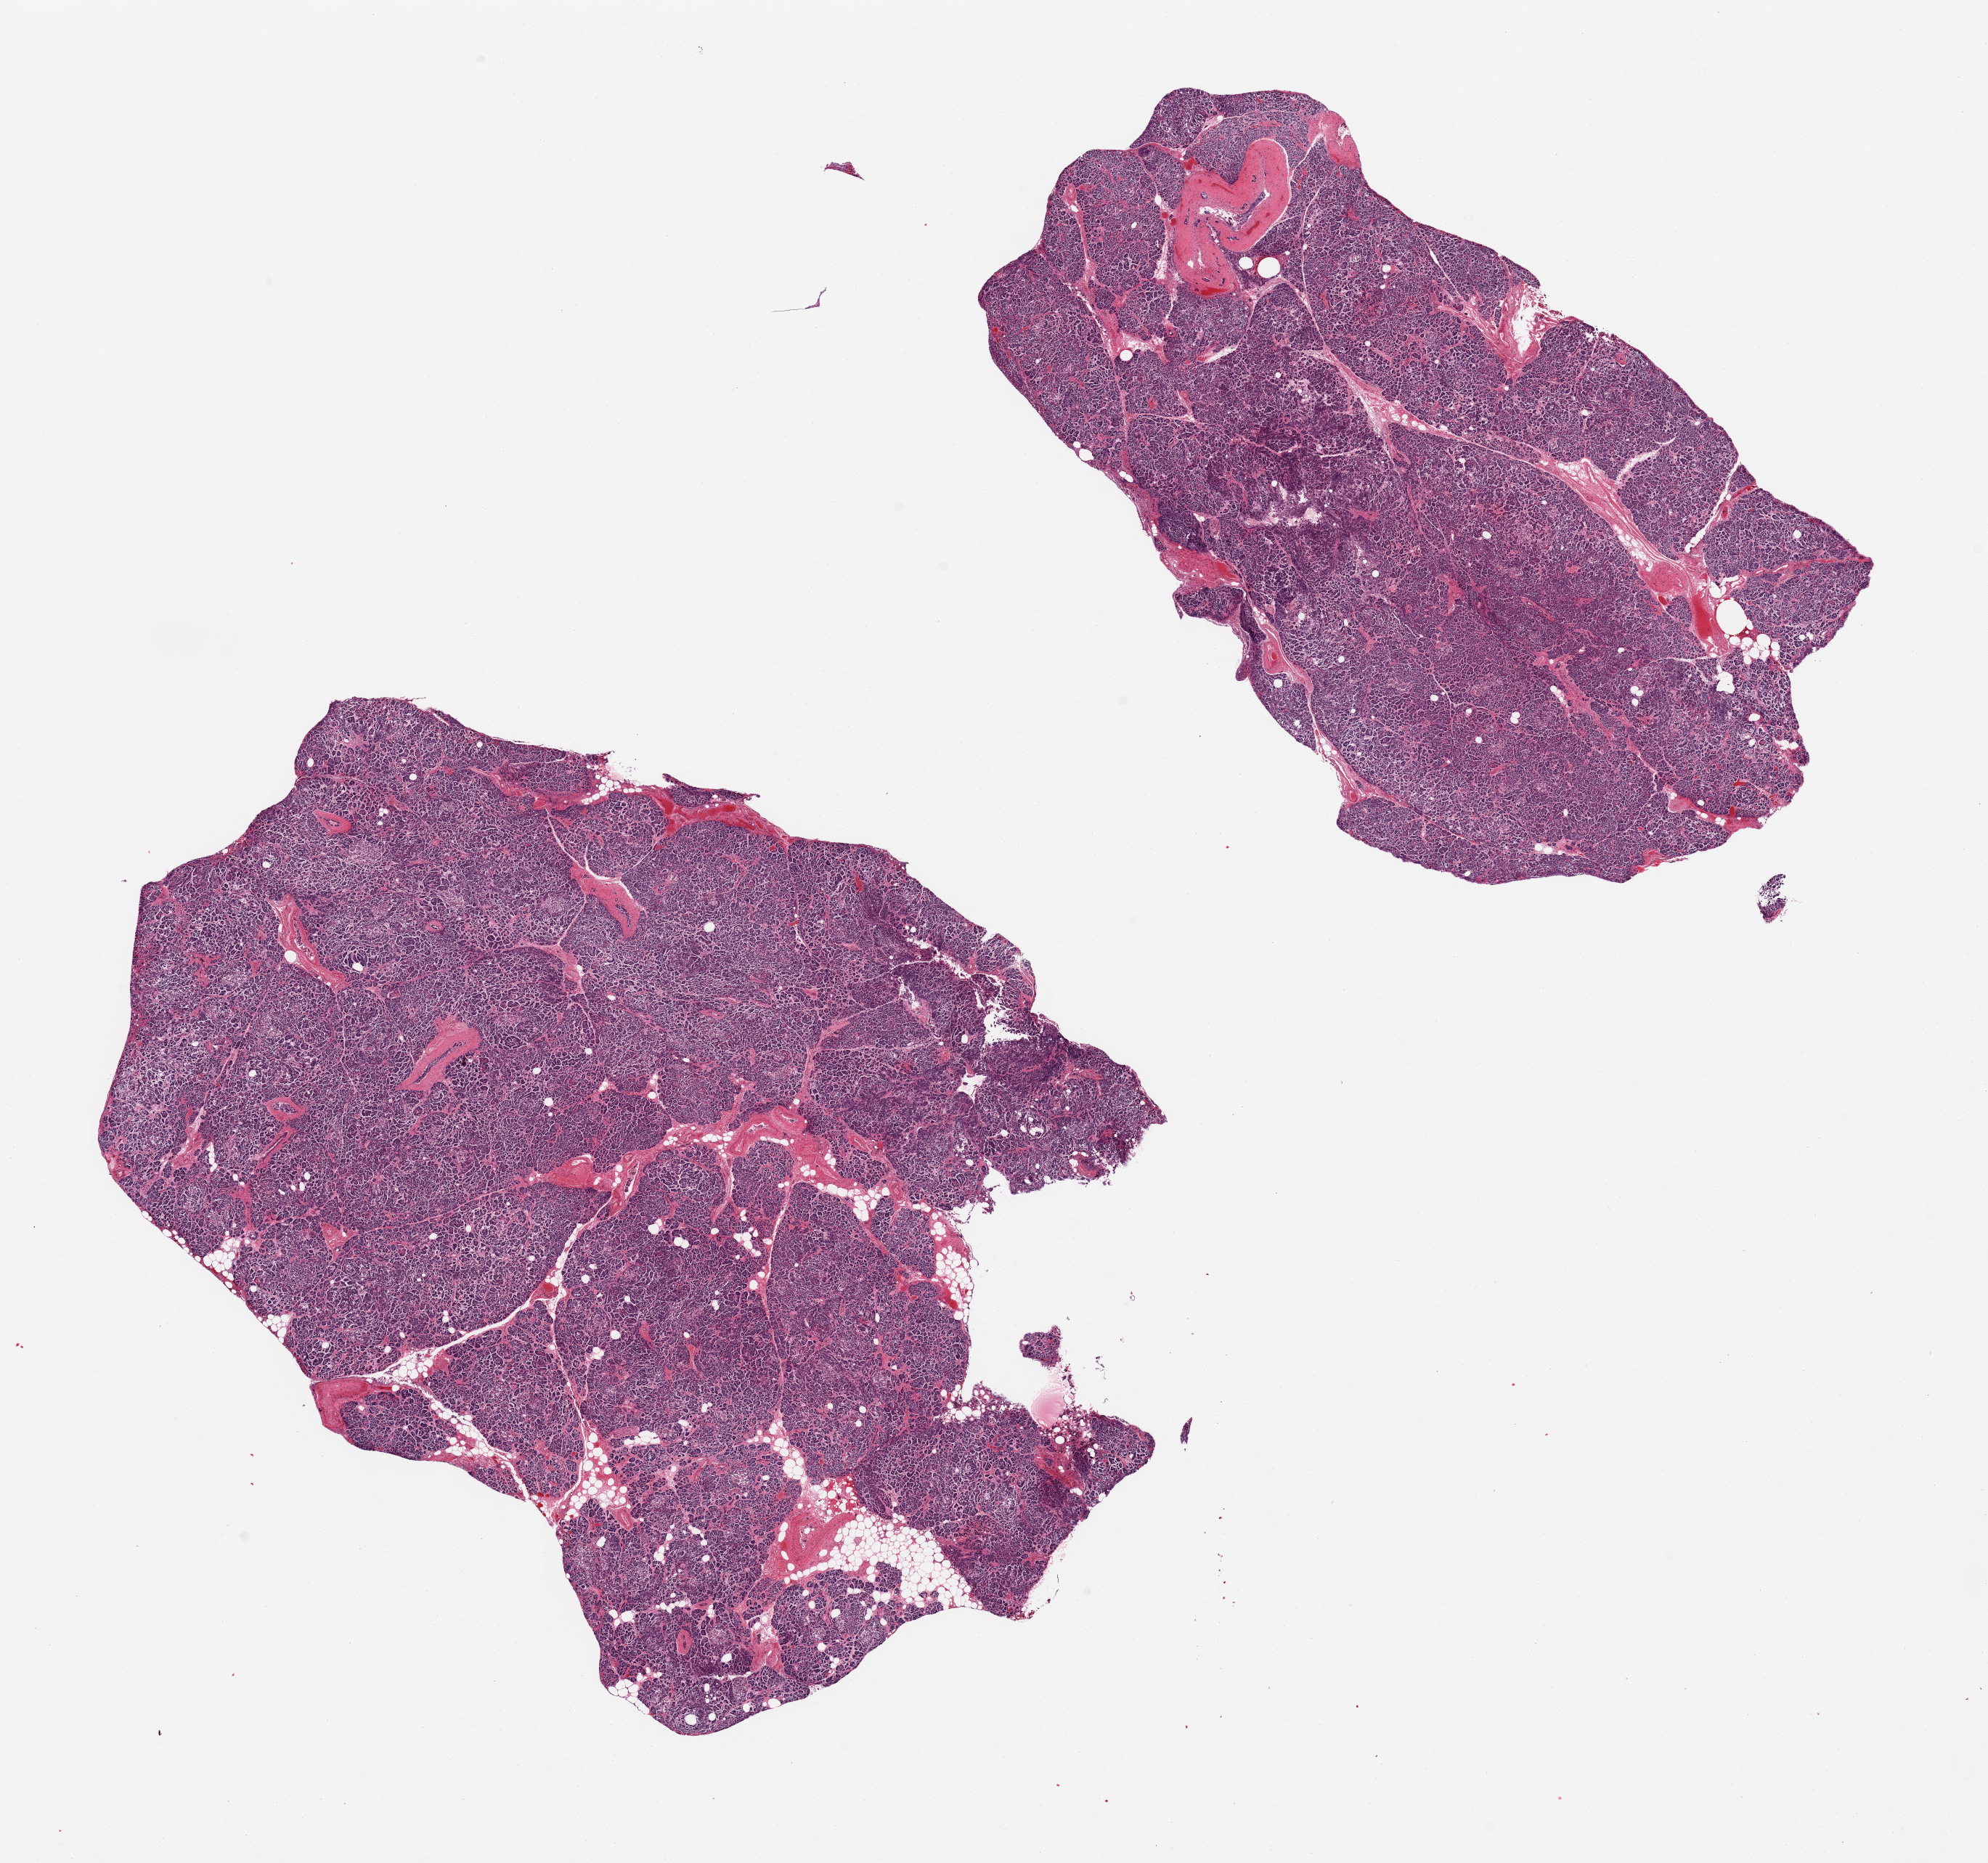
Digitized haematoxylin and eosin-stained section — shown as a low-resolution overview of the whole scanned area (about 21.7 x 20.3 mm). PAXgene-fixed, paraffin-embedded tissue. Target tissue: pancreas. Donor tissue sample. Donor sex: female.
* review note (as recorded): 2 pieces, moderate-marked autolysis/saponification. Islets not well visualized. Minimal fat